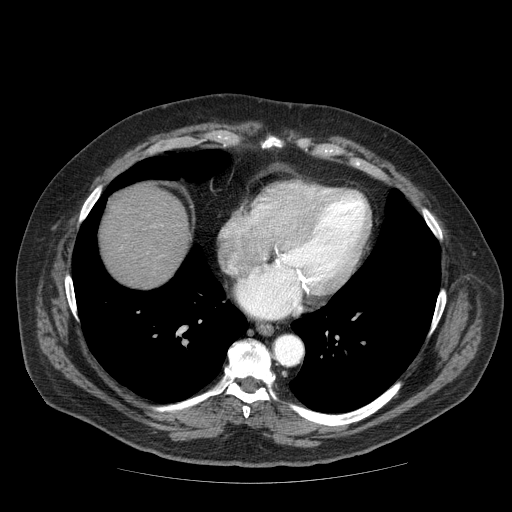
Contrast-enhanced abdominal CT (liver protocol), one axial slice. Slice 70 of 85 in the series (ordered by position). 120 kVp. Soft-tissue window (W 400 / L 40 HU). 2.5 mm slice thickness. 512 × 512 image matrix. From the clinical record (not read from this slice): diagnosis: hepatocellular carcinoma (patient treated with transarterial chemoembolisation; whether this scan precedes or follows treatment is not stated here); TNM stage (as recorded): Stage-IIIA; Child-Pugh class: A; tumour nodularity: multinodular.
Outlined on this slice (semi-automatic segmentation, software-assisted and operator-edited):
- liver parenchyma outside the tumour (the mass and vessels are separate outlines, so this box may not span the whole liver): box from (x=100, y=184) to (x=190, y=288) px